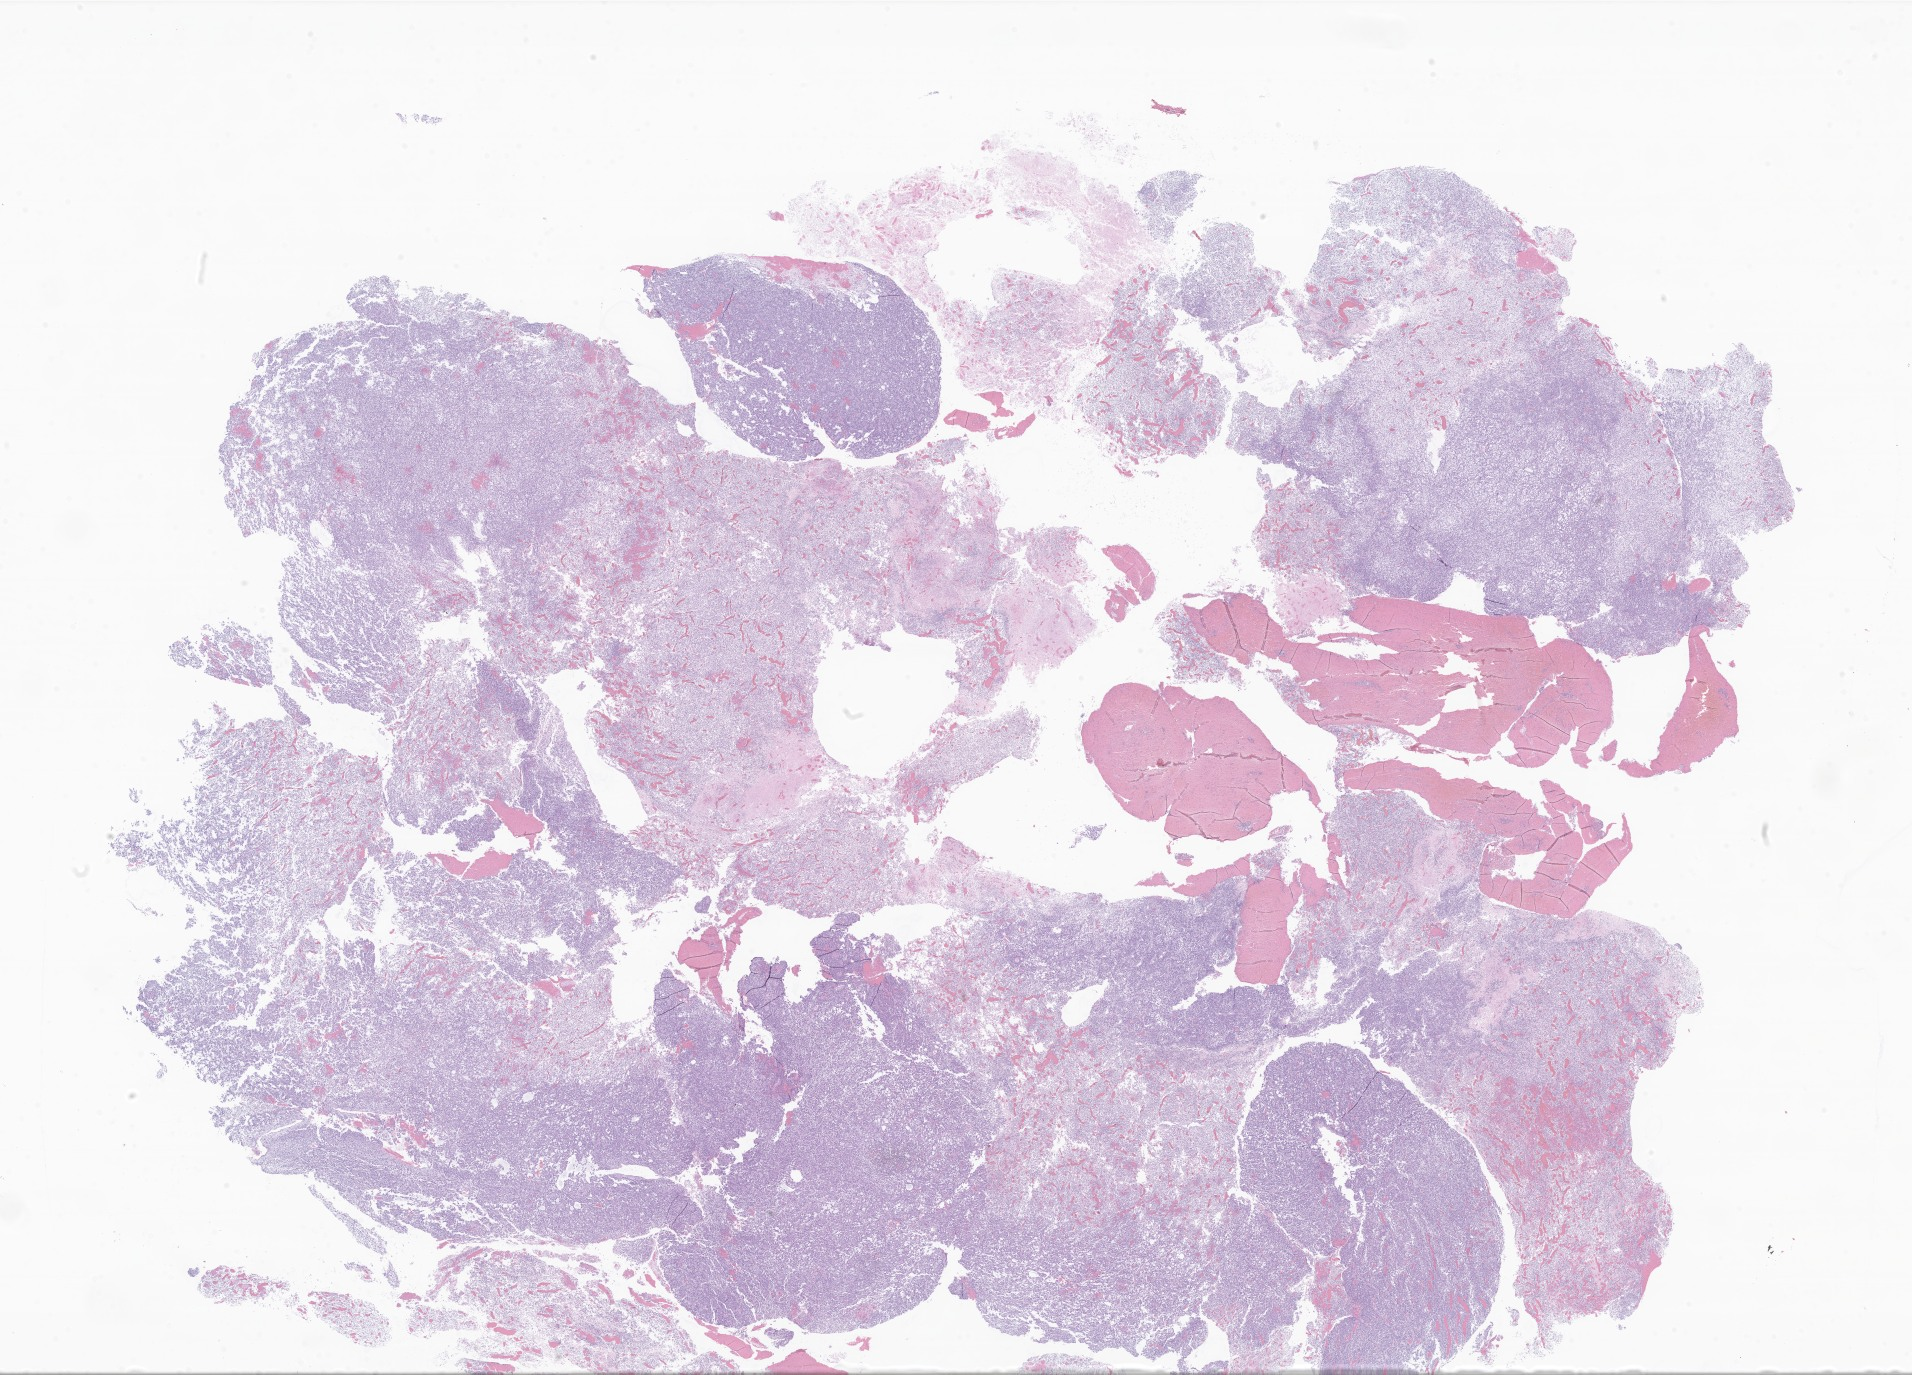
Hematoxylin and eosin (H&E) whole-slide image of tumor tissue from the brain, whole scanned area (about 32.2 x 23.2 mm) shown as a low-resolution overview, FFPE section. Patient: female, age 665 days.
Diagnosis (ICD-O-3 morphology term): Glioma, malignant.